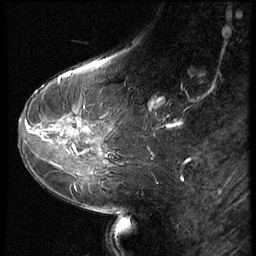
Breast MRI (dynamic contrast-enhanced), one sagittal slice. 3 images stored at this slice position (order not interpretable as contrast timing). 1.5 T. TE 4.2 ms, TR 9 ms. 2.5 mm slice thickness. 256 × 256 image matrix, field of view 180 × 180 mm. Patient: female, 54 years. Case-level facts recorded for this patient, not image findings: setting: breast cancer imaged before/during neoadjuvant chemotherapy; receptor status: HR-positive, HER2-negative.
Annotated regions visible in this slice (semi-automatically segmented with operator editing):
- analysis volume of interest (the breast-tissue region the enhancement analysis was run in; not a lesion): bounding box <24,110,94,159> (left, top, right, bottom; pixels)
- tumour enhancement mask (voxels above the 140 % enhancement threshold inside the analysis volume of interest): <27,123,81,132>